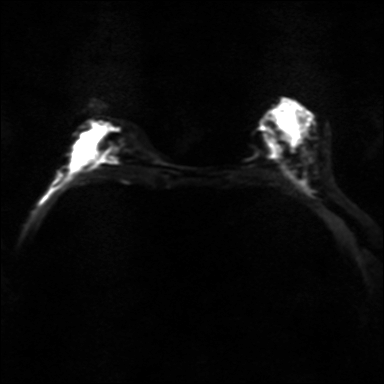
Breast MRI, one axial slice. Diffusion-weighted series; image 2 of 4 stored at this slice position (different b-values; order by instance number). 3 T. 384 × 384 image matrix, field of view 320 × 320 mm. Female patient.
Annotated regions visible in this slice (manually delineated by an expert):
- tumour on diffusion-weighted imaging: bounding box [x1, y1, x2, y2] px = [103, 142, 120, 163]